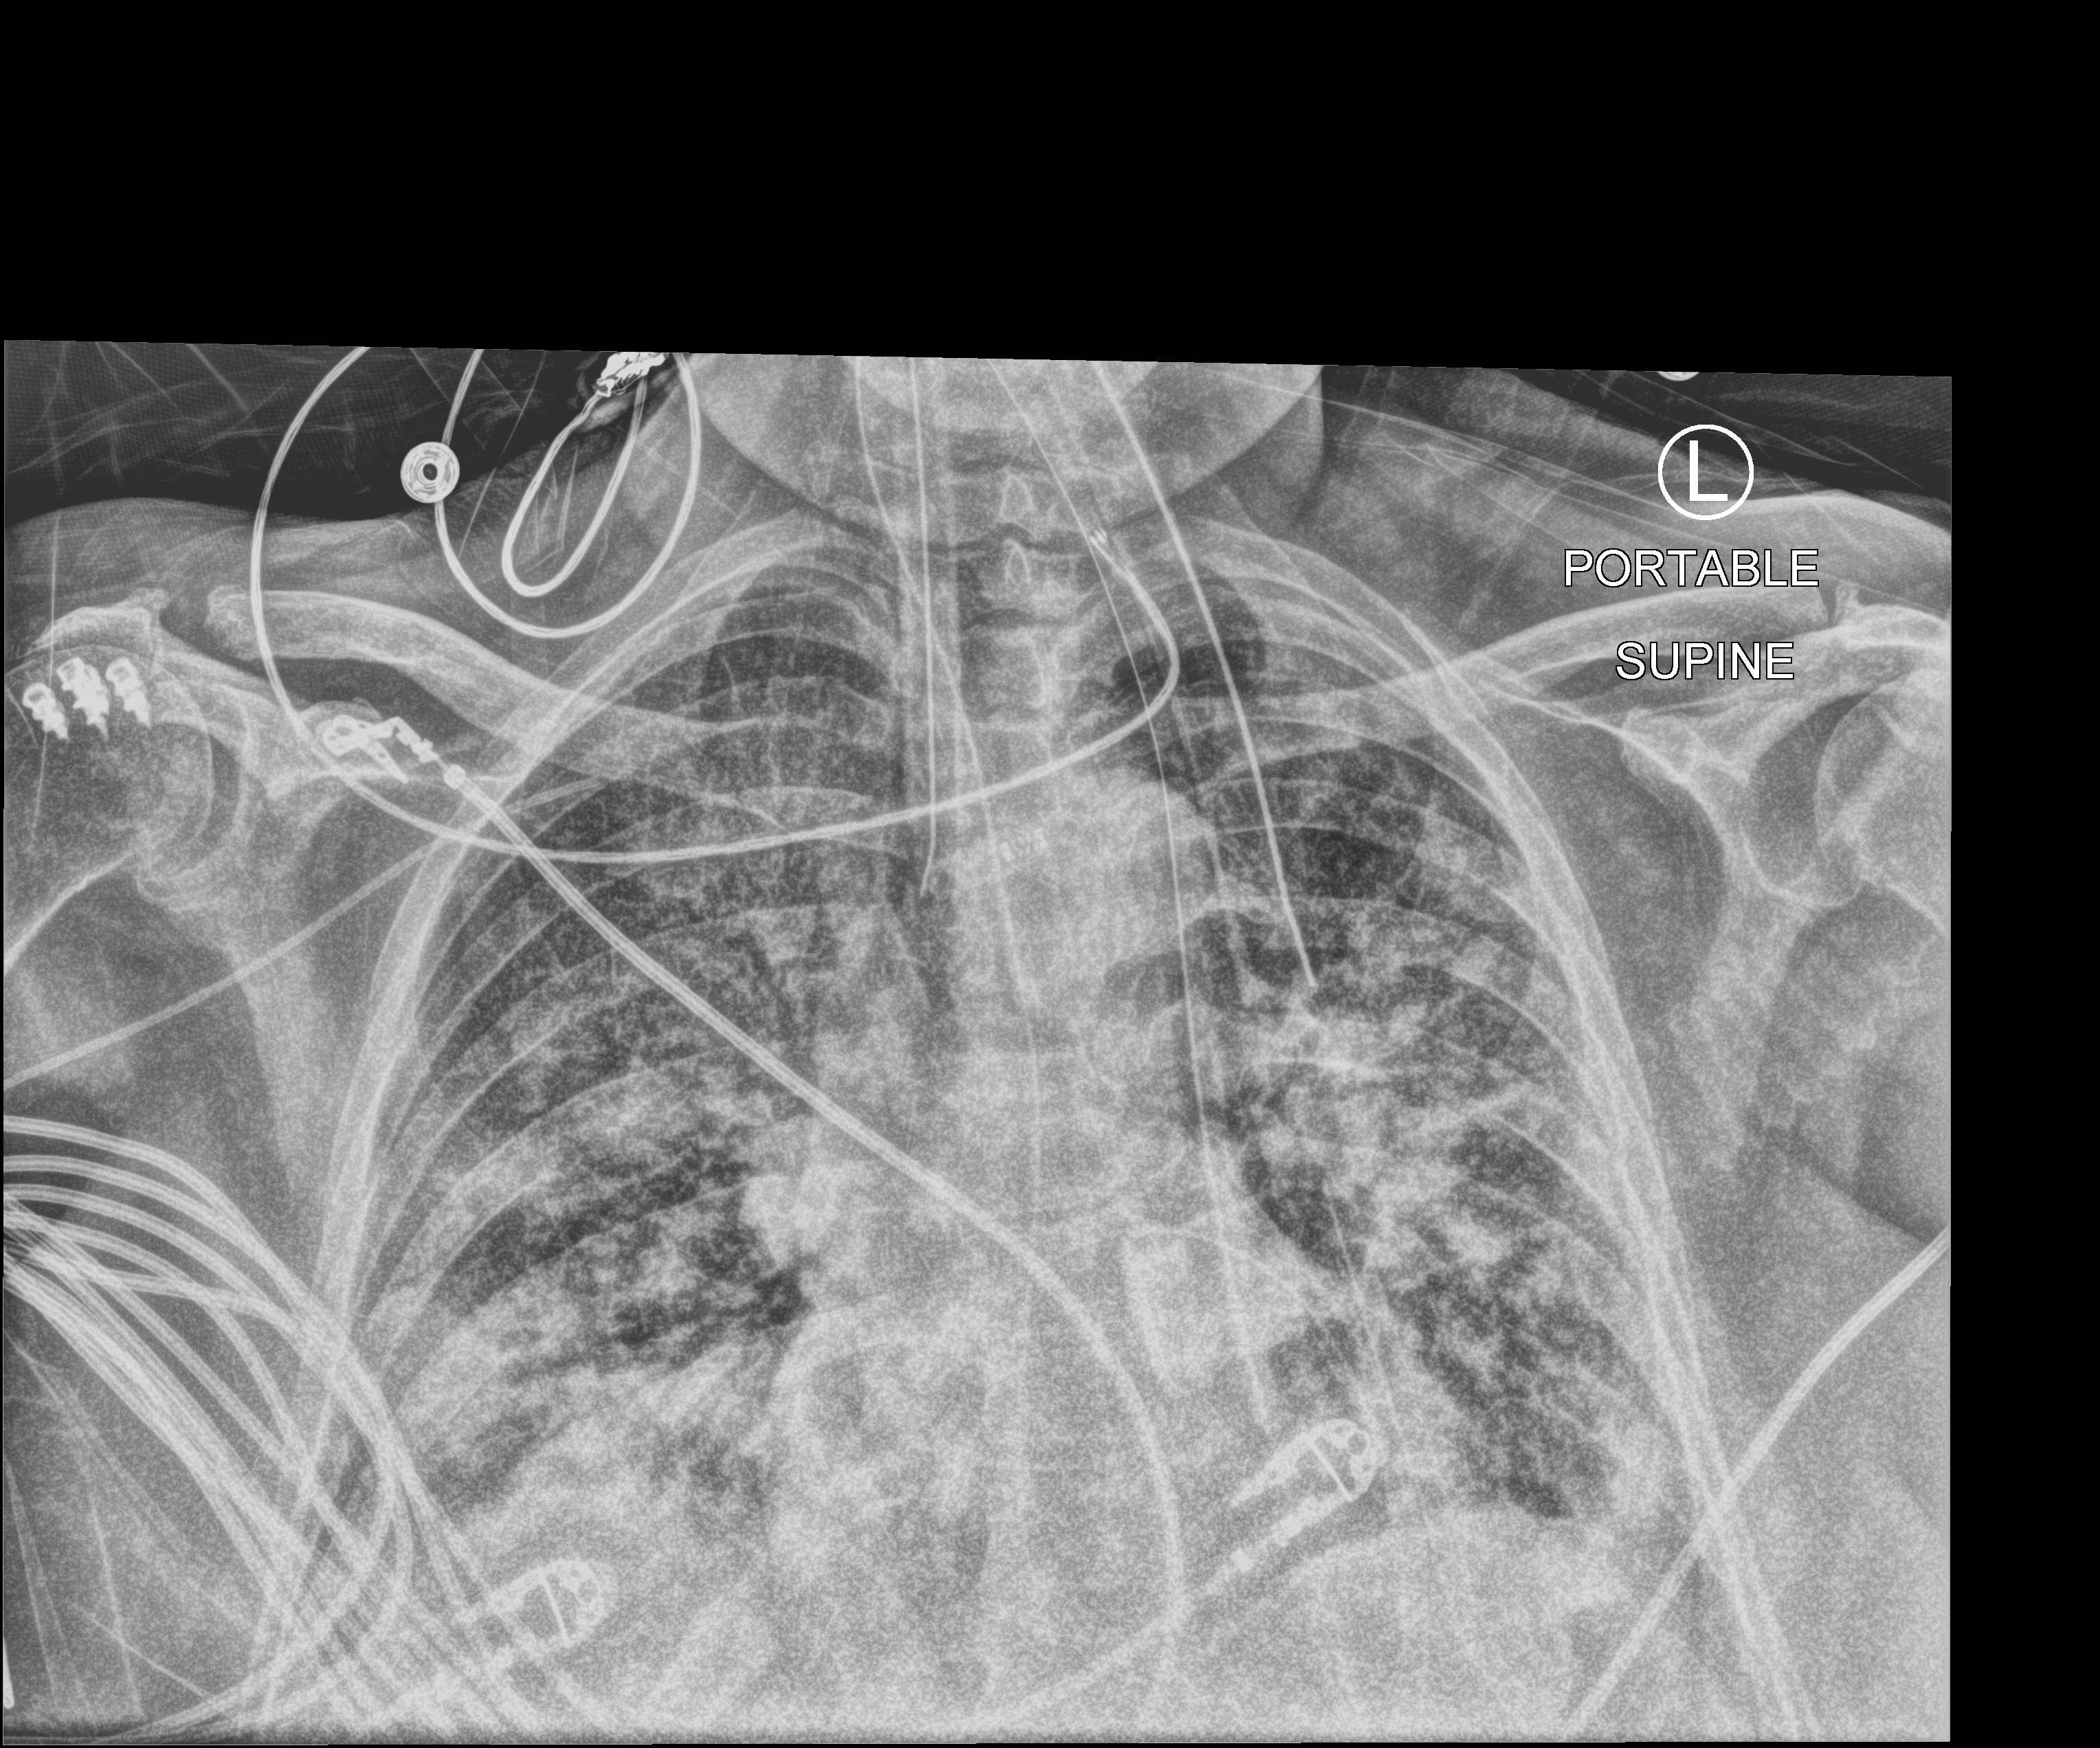
Bedside chest radiograph (computed radiography), anteroposterior (AP) projection. Patient hospitalised with COVID-19; female, aged 60–74 years.
From the hospital-stay record, not from the radiograph (when in the stay this image was taken is not recorded): other chronic lung disease (admission record): no.